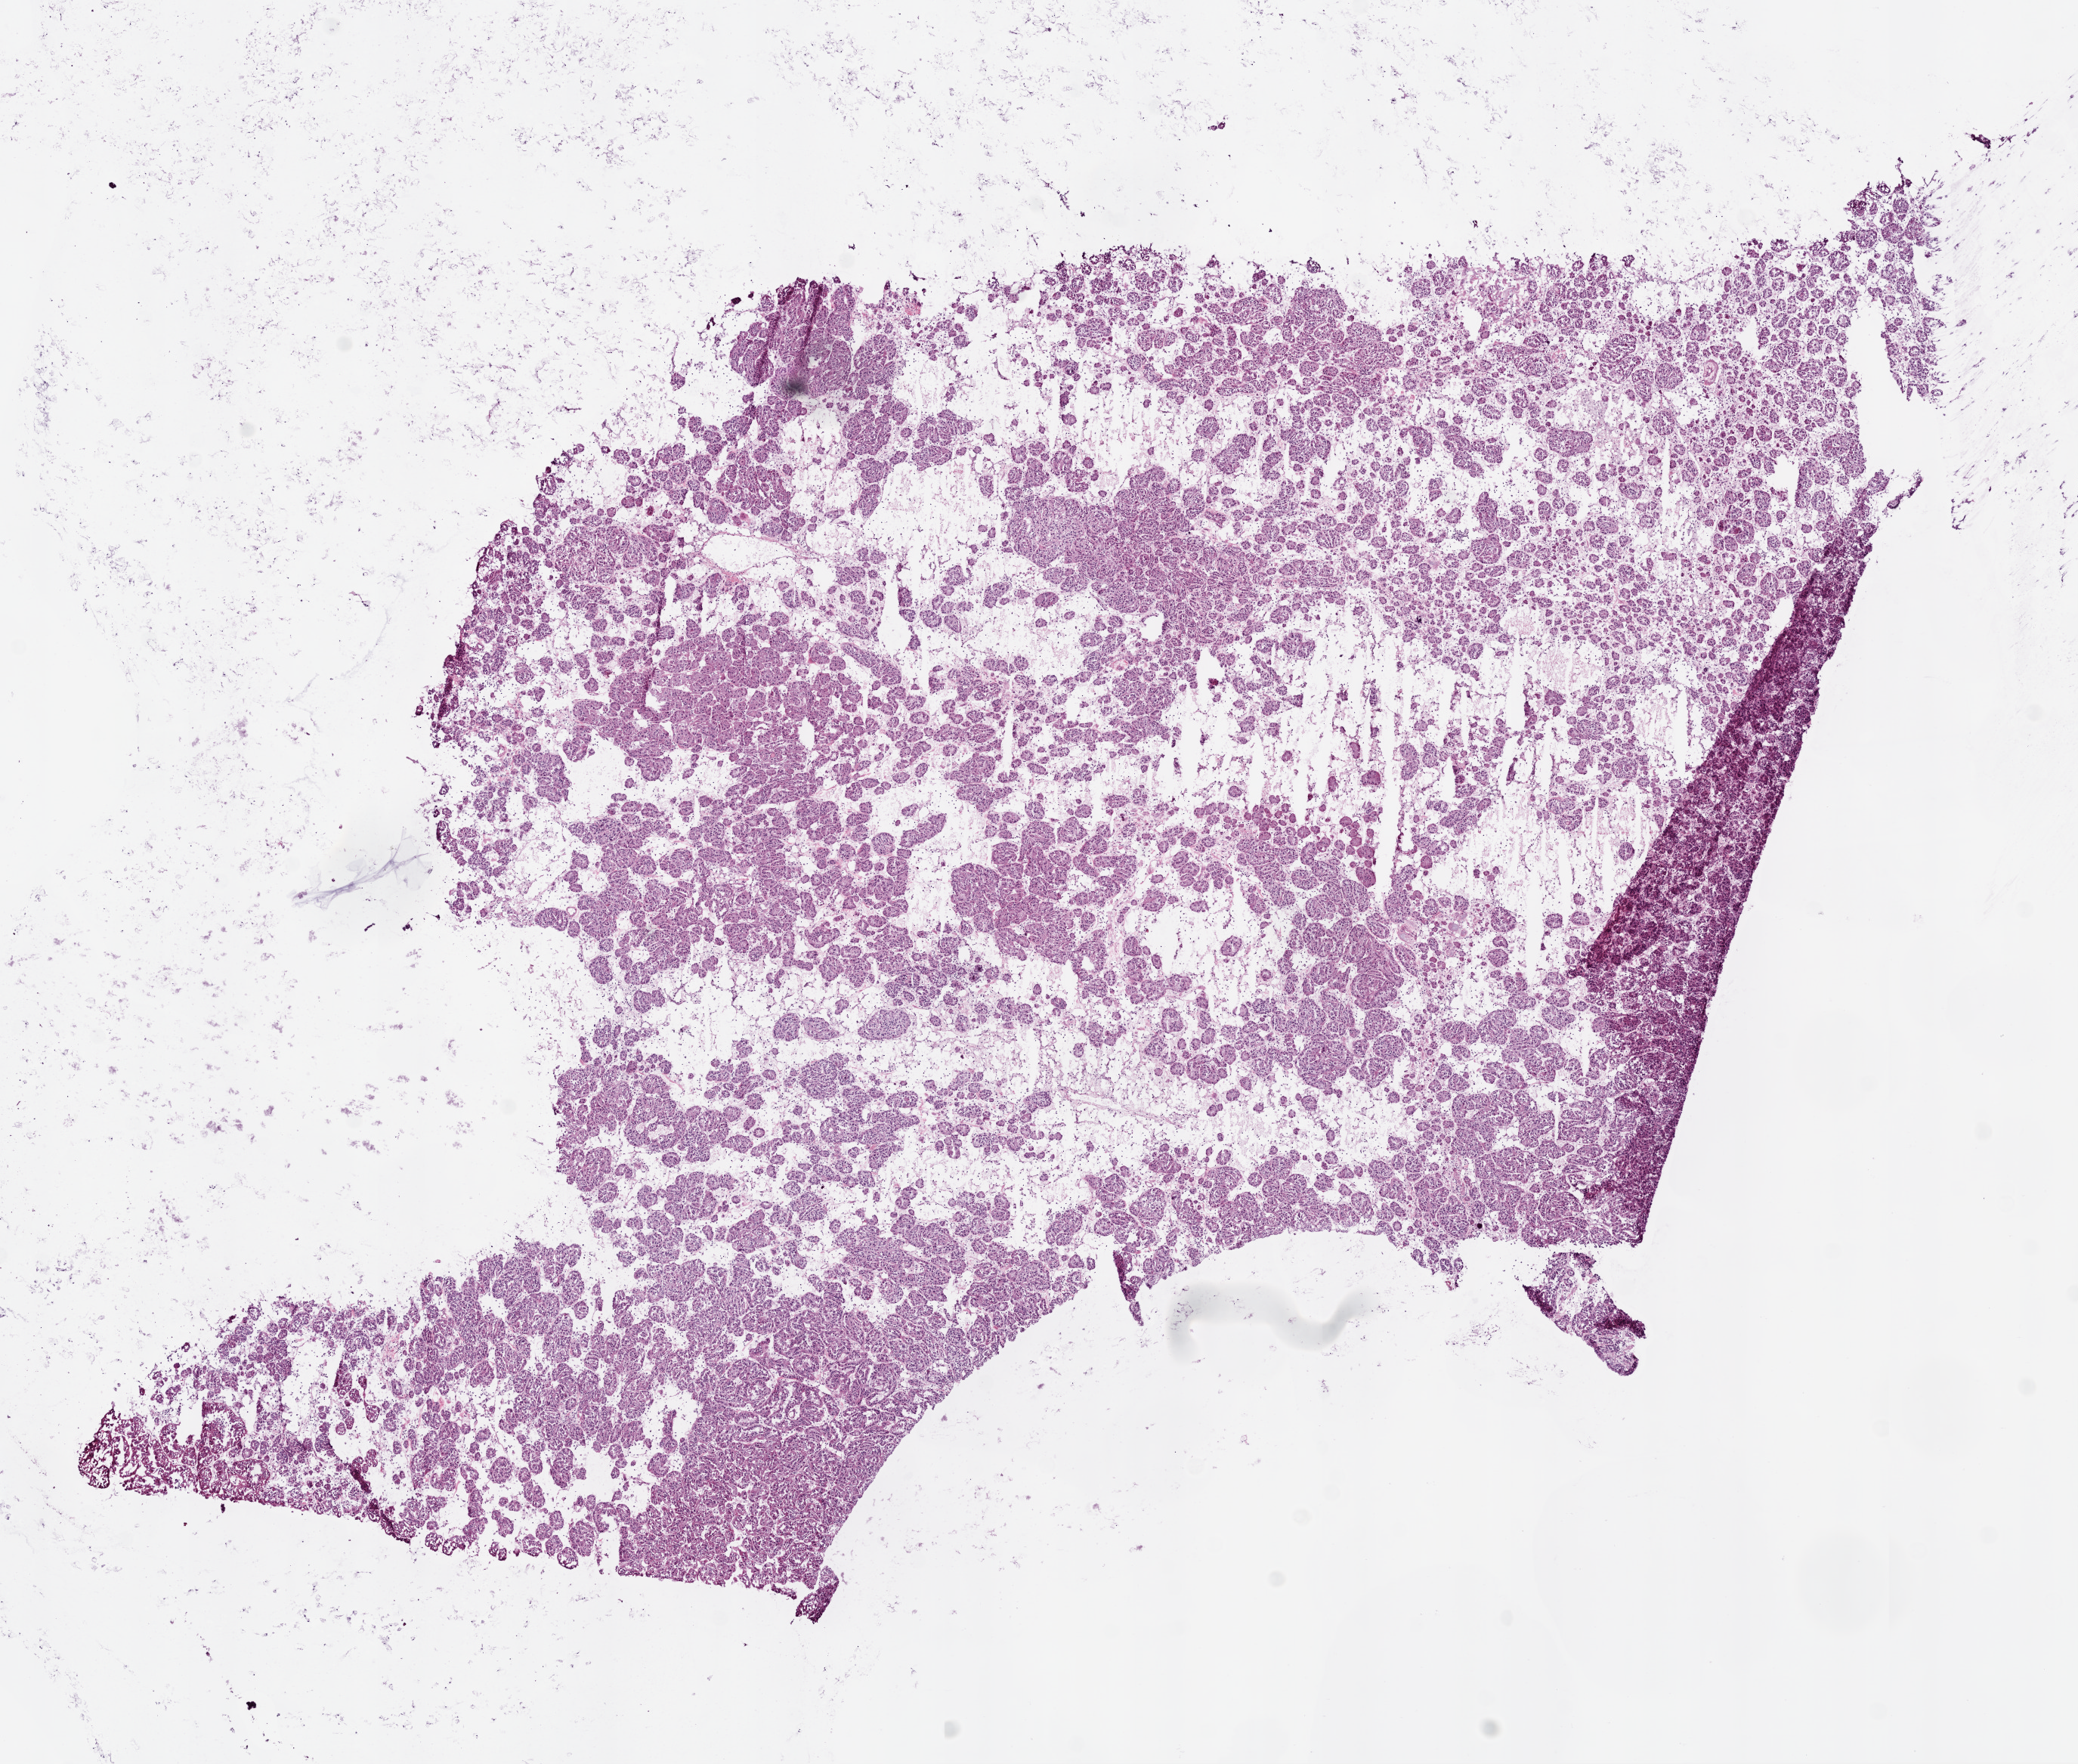
Digitized H&E tissue section (whole slide) — low-resolution overview of the scanned area, about 11.0 x 9.4 mm. Frozen section. Sample: primary tumour, kidney. Patient: female, age at initial diagnosis 48 years. Composition of this section per pathologist review: tumour cells 80%, tumour nuclei 80%, normal cells 0%, stromal cells 20%, necrosis 0%.
Pathologic diagnosis: Papillary adenocarcinoma, NOS.